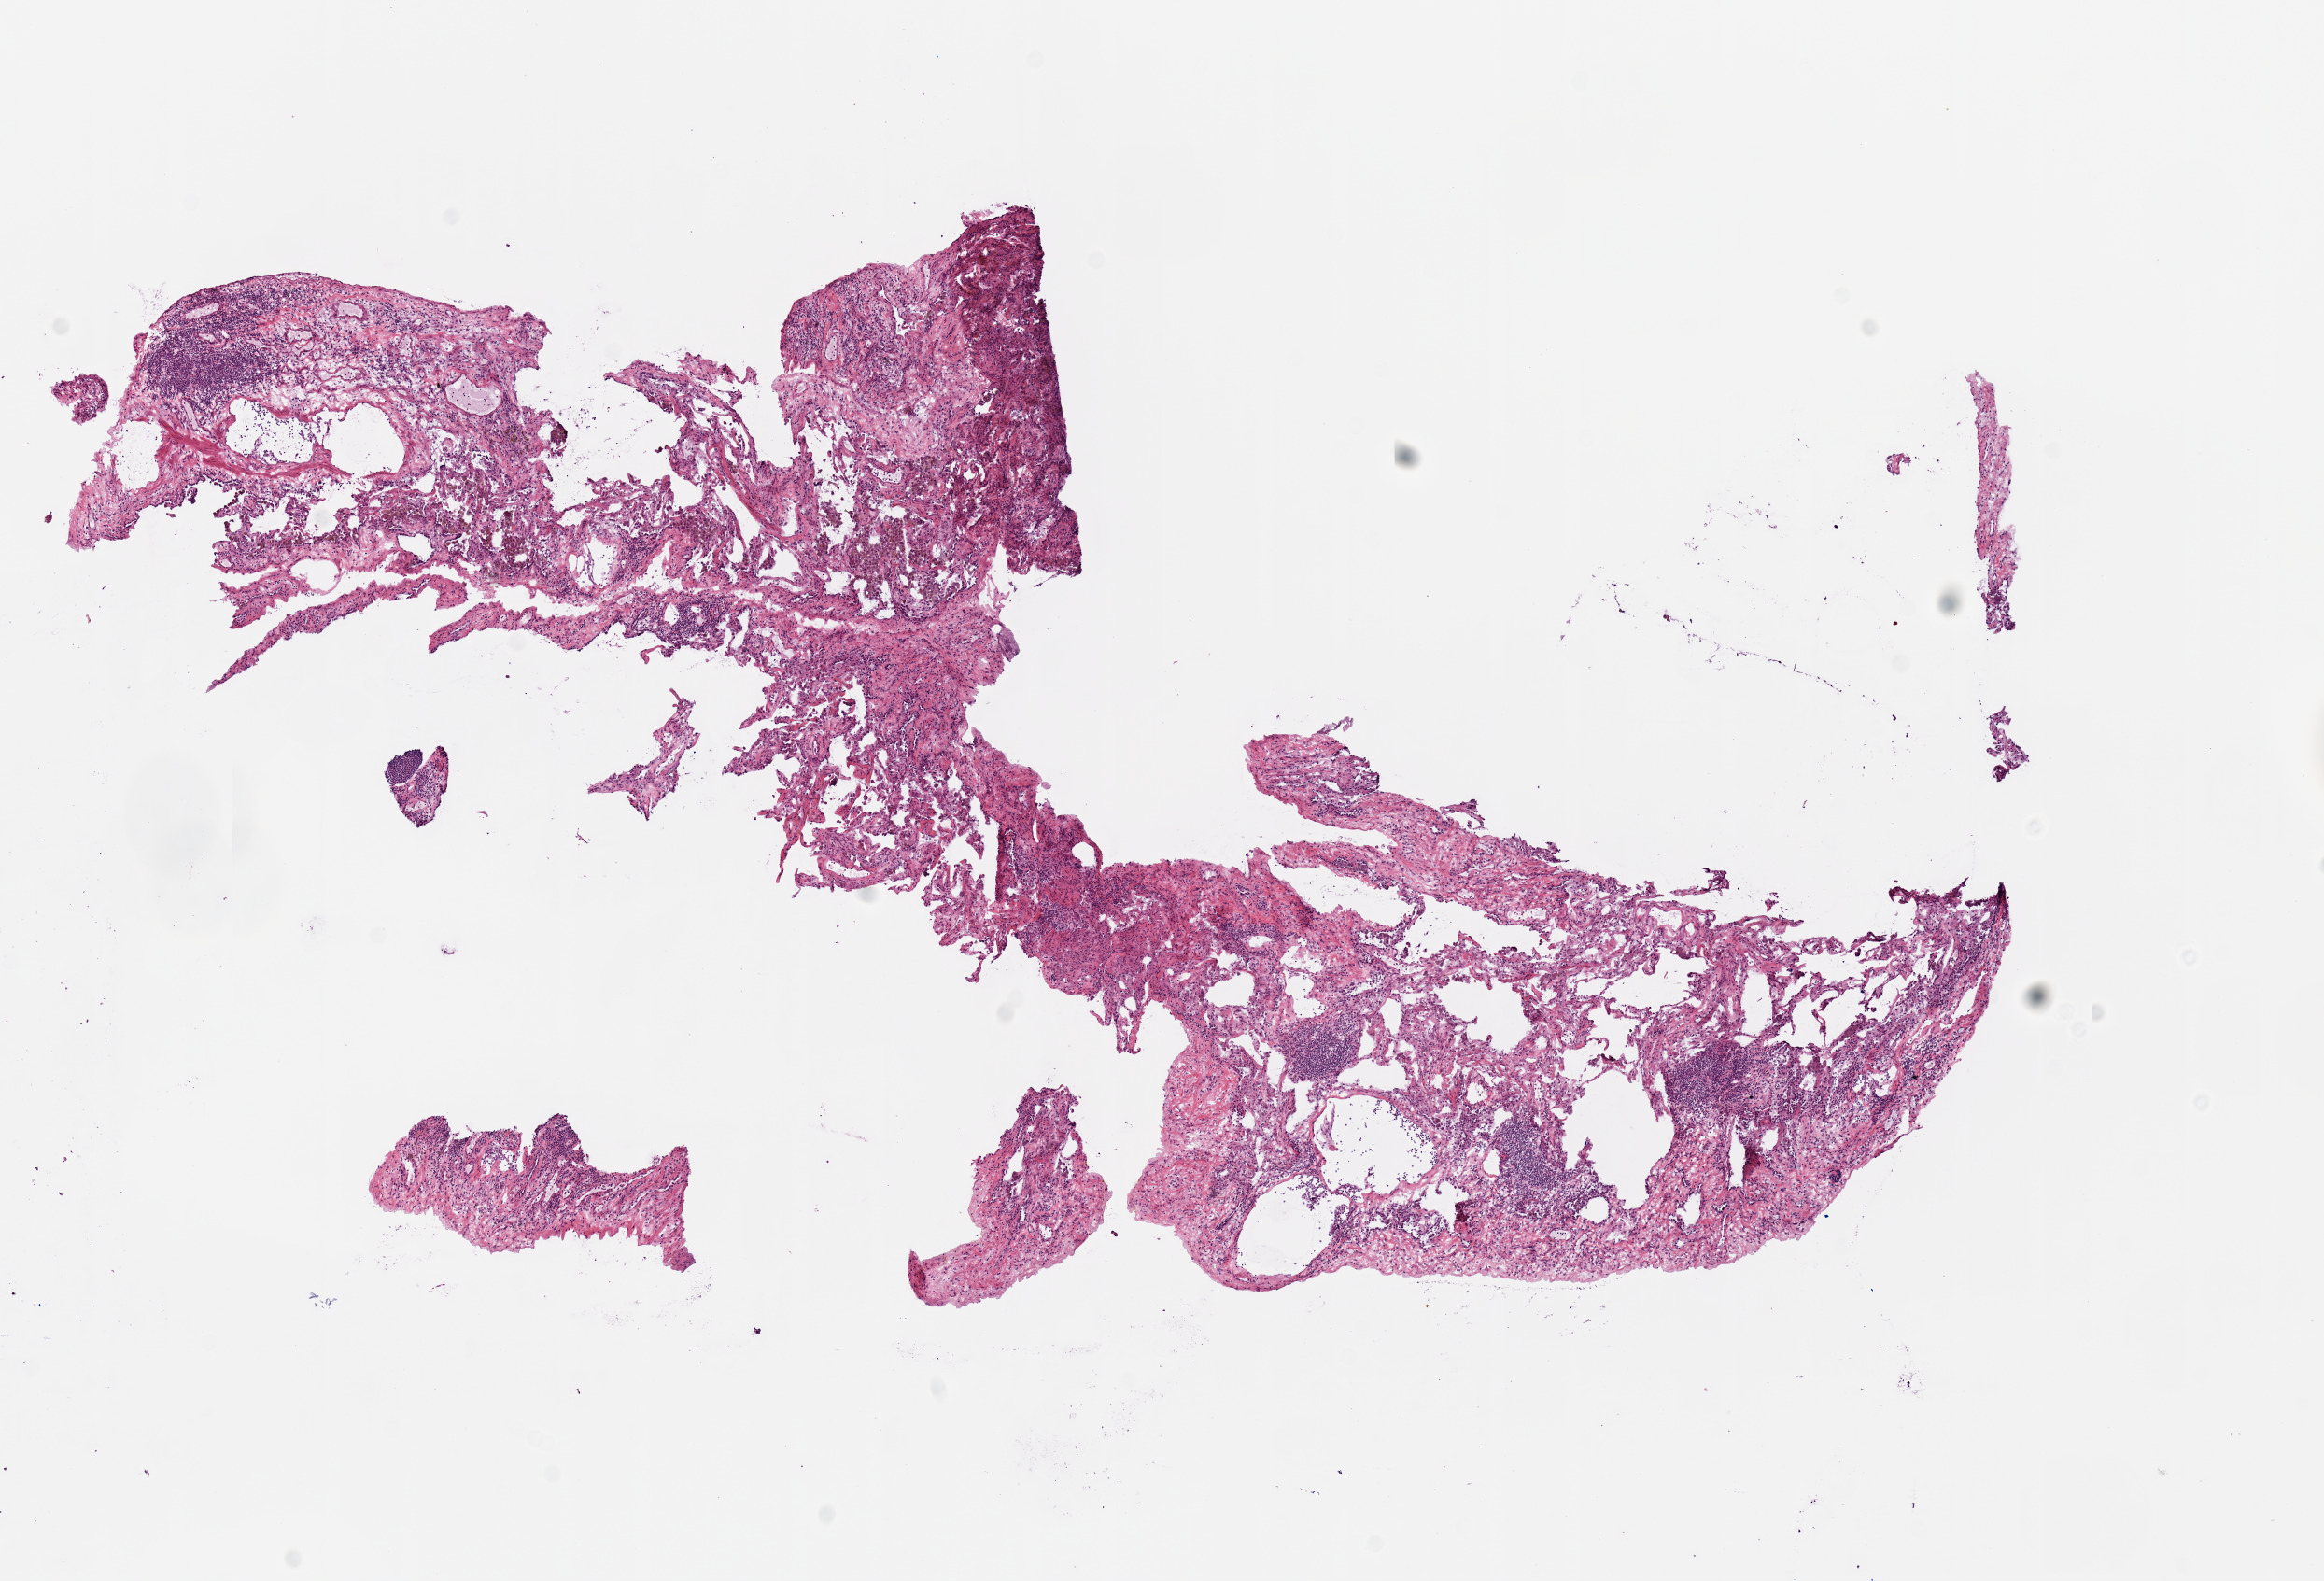
Whole-slide histology image, H&E-stained, shown as a low-resolution overview of the whole scanned area (about 9.8 x 6.7 mm, from a 20x scan), frozen section from the top of the tissue portion, sample: solid tissue normal (non-tumour tissue), lung. Male, age 61 years at initial diagnosis.
This section: solid tissue normal sample (biorepository sample class). Patient diagnosis: Adenocarcinoma, NOS (lower lobe, lung).